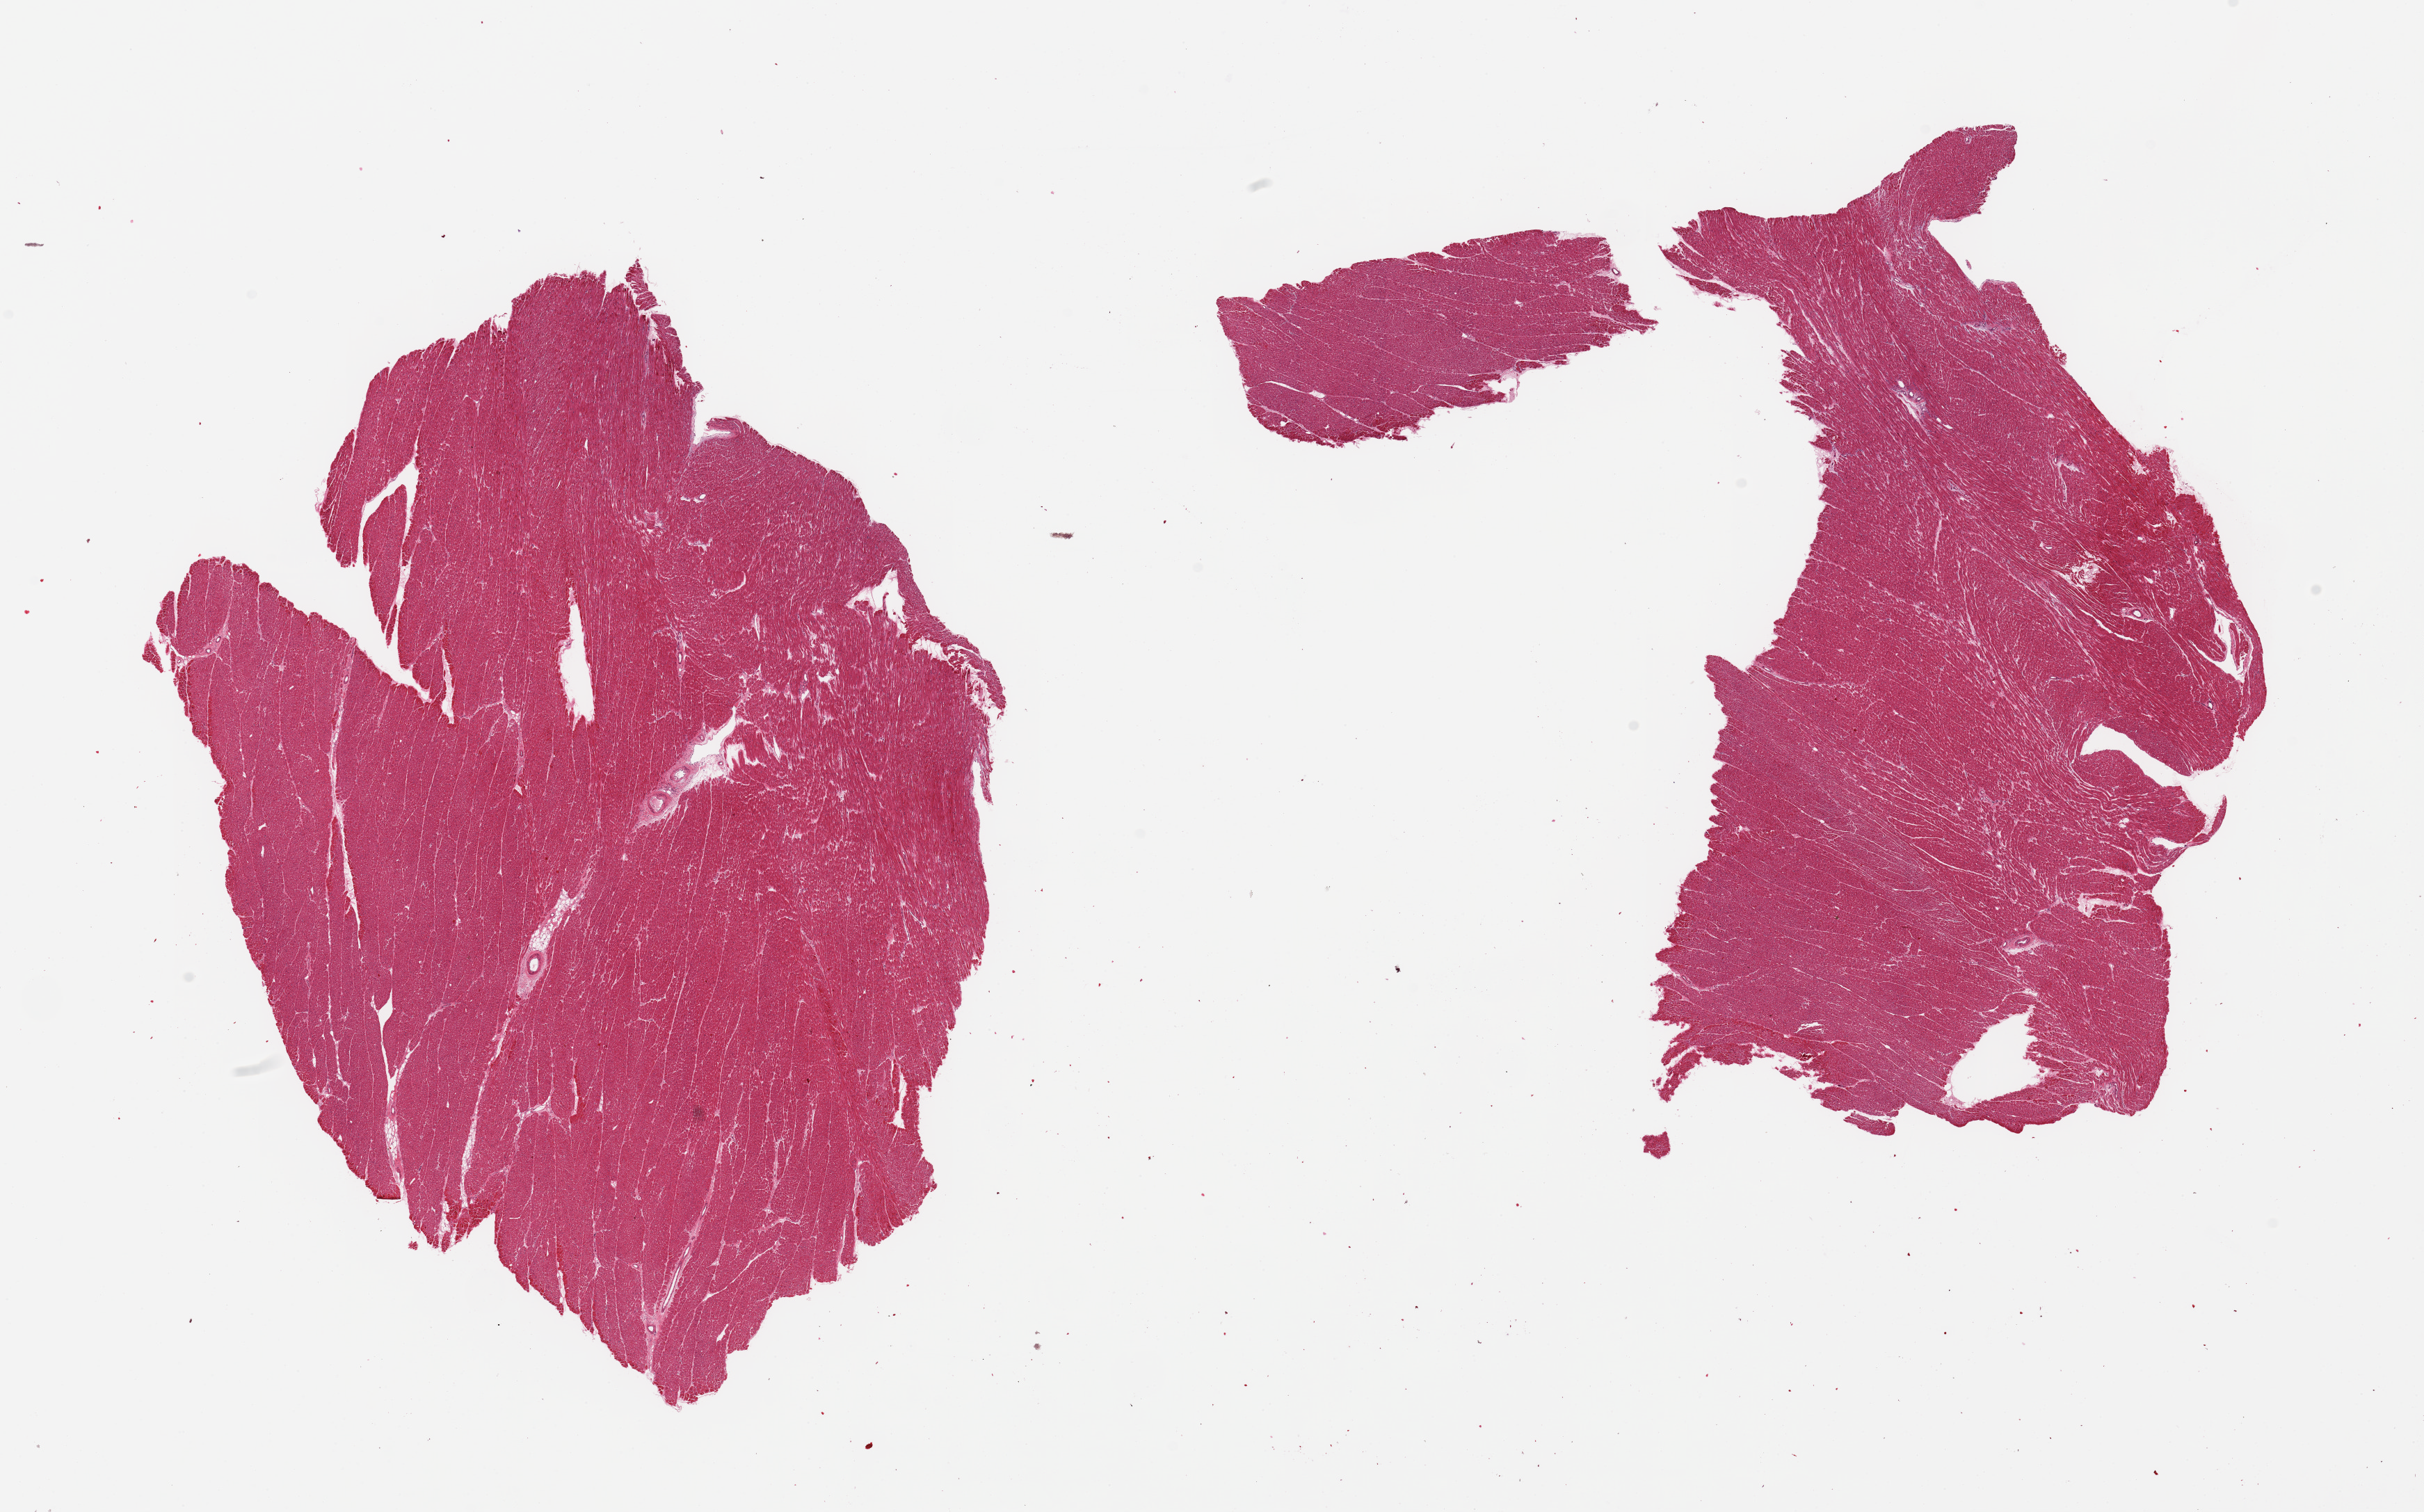
Whole-slide image, H&E stain — low-resolution overview of the scanned area, about 27.6 x 17.2 mm; PAXgene-fixed, paraffin-embedded tissue; section of heart (target tissue); donor tissue sample. Female donor.
- reviewer comment on this tissue sample: 2 pieces, no significant interstitial fibrosis